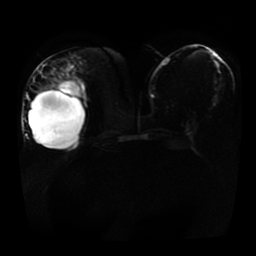
Breast MRI, one axial slice; slice 17 of 41 in the series (ordered by position); diffusion-weighted series; image 2 of 4 stored at this slice position (different b-values; order by instance number); 1.5 T; 5 mm slice thickness; 256 × 256 image matrix, field of view 360 × 360 mm. Female patient.
Annotated regions visible in this slice (manually delineated by an expert):
- tumour on diffusion-weighted imaging: bounding box [x1, y1, x2, y2] px = [57, 79, 84, 100]